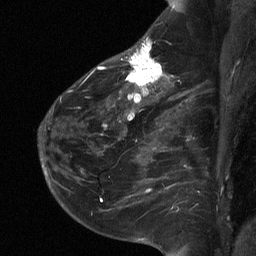
Breast MRI (dynamic contrast-enhanced), one sagittal slice; position 43 of 64 along the scan axis; dynamic contrast-enhanced study with each time point stored as its own series, time point 2 of 3 at this slice position (early post-contrast, ordered by acquisition time); 1.5 T; TE 4.8 ms, TR 27 ms; 2 mm slice thickness; 256 × 256 image matrix, field of view 180 × 180 mm. Female patient, age 51 years. From the clinical record (not read from this slice): setting: breast cancer imaged before/during neoadjuvant chemotherapy; receptor status: HR-positive, HER2-negative.
Structures marked on this image (semi-automatic segmentation, software-assisted and operator-edited):
- analysis volume of interest (the breast-tissue region the enhancement analysis was run in; not a lesion): bounding box [x1, y1, x2, y2] px = [72, 34, 182, 118]
- tumour enhancement mask (voxels above the 90 % enhancement threshold inside the analysis volume of interest): [97, 39, 163, 118]